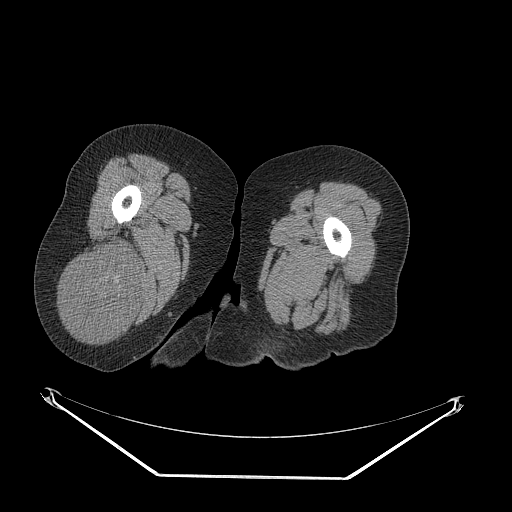
CT of an extremity soft-tissue mass (from a PET/CT study), one axial slice. Slice 38 of 257 in the series (ordered by position). Reconstruction kernel STANDARD. 140 kVp. Soft-tissue window (W 400 / L 40 HU). 3.75 mm slice thickness. 512 × 512 image matrix. Female patient. Case-level facts recorded for this patient, not image findings: histological type: synovial sarcoma; grade: intermediate; site of the primary tumour: right buttock.
Annotated regions visible in this slice (expert contour drawn on MRI and transferred to this co-registered scan by the dataset authors):
- gross tumour volume including surrounding oedema: bounding box <62,242,143,339> (left, top, right, bottom; pixels)
- gross tumour volume (mass): <62,246,143,339>